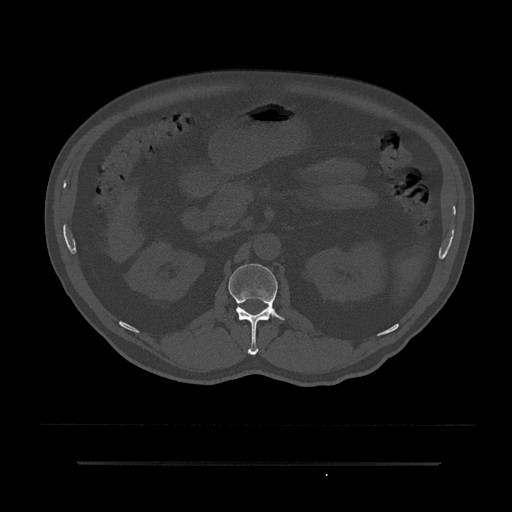
CT including the spine, one axial slice. Position 140 of 797 along the scan axis. Reconstruction kernel Br40s/3. Bone window (W 1800 / L 400 HU). 0.5 mm slice thickness. 512 × 512 image matrix. Male patient, age 59 years. Case-level facts recorded for this patient, not image findings: primary cancer: bile ducts; vertebrae with lytic lesions (as recorded): T10.
Annotated regions visible in this slice (semi-automatically segmented with operator editing):
- L1 vertebra: box from (x=229, y=264) to (x=285, y=355) px